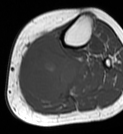
MRI of an extremity soft-tissue mass, one axial slice. Position 32 of 68 along the scan axis. MR volume resampled by the dataset authors to the PET/CT grid (not the native acquisition matrix). 3.27 mm slice thickness. 123 × 134 image matrix, field of view 120 × 131 mm. Female patient. From the clinical record (not read from this slice): histological type: extraskeletal high grade osteogenic sarcoma; grade: high; site of the primary tumour: left calf.
Annotated regions visible in this slice (expert contour drawn on MRI and transferred to this co-registered scan by the dataset authors):
- gross tumour volume (mass): box from (x=20, y=36) to (x=78, y=101) px